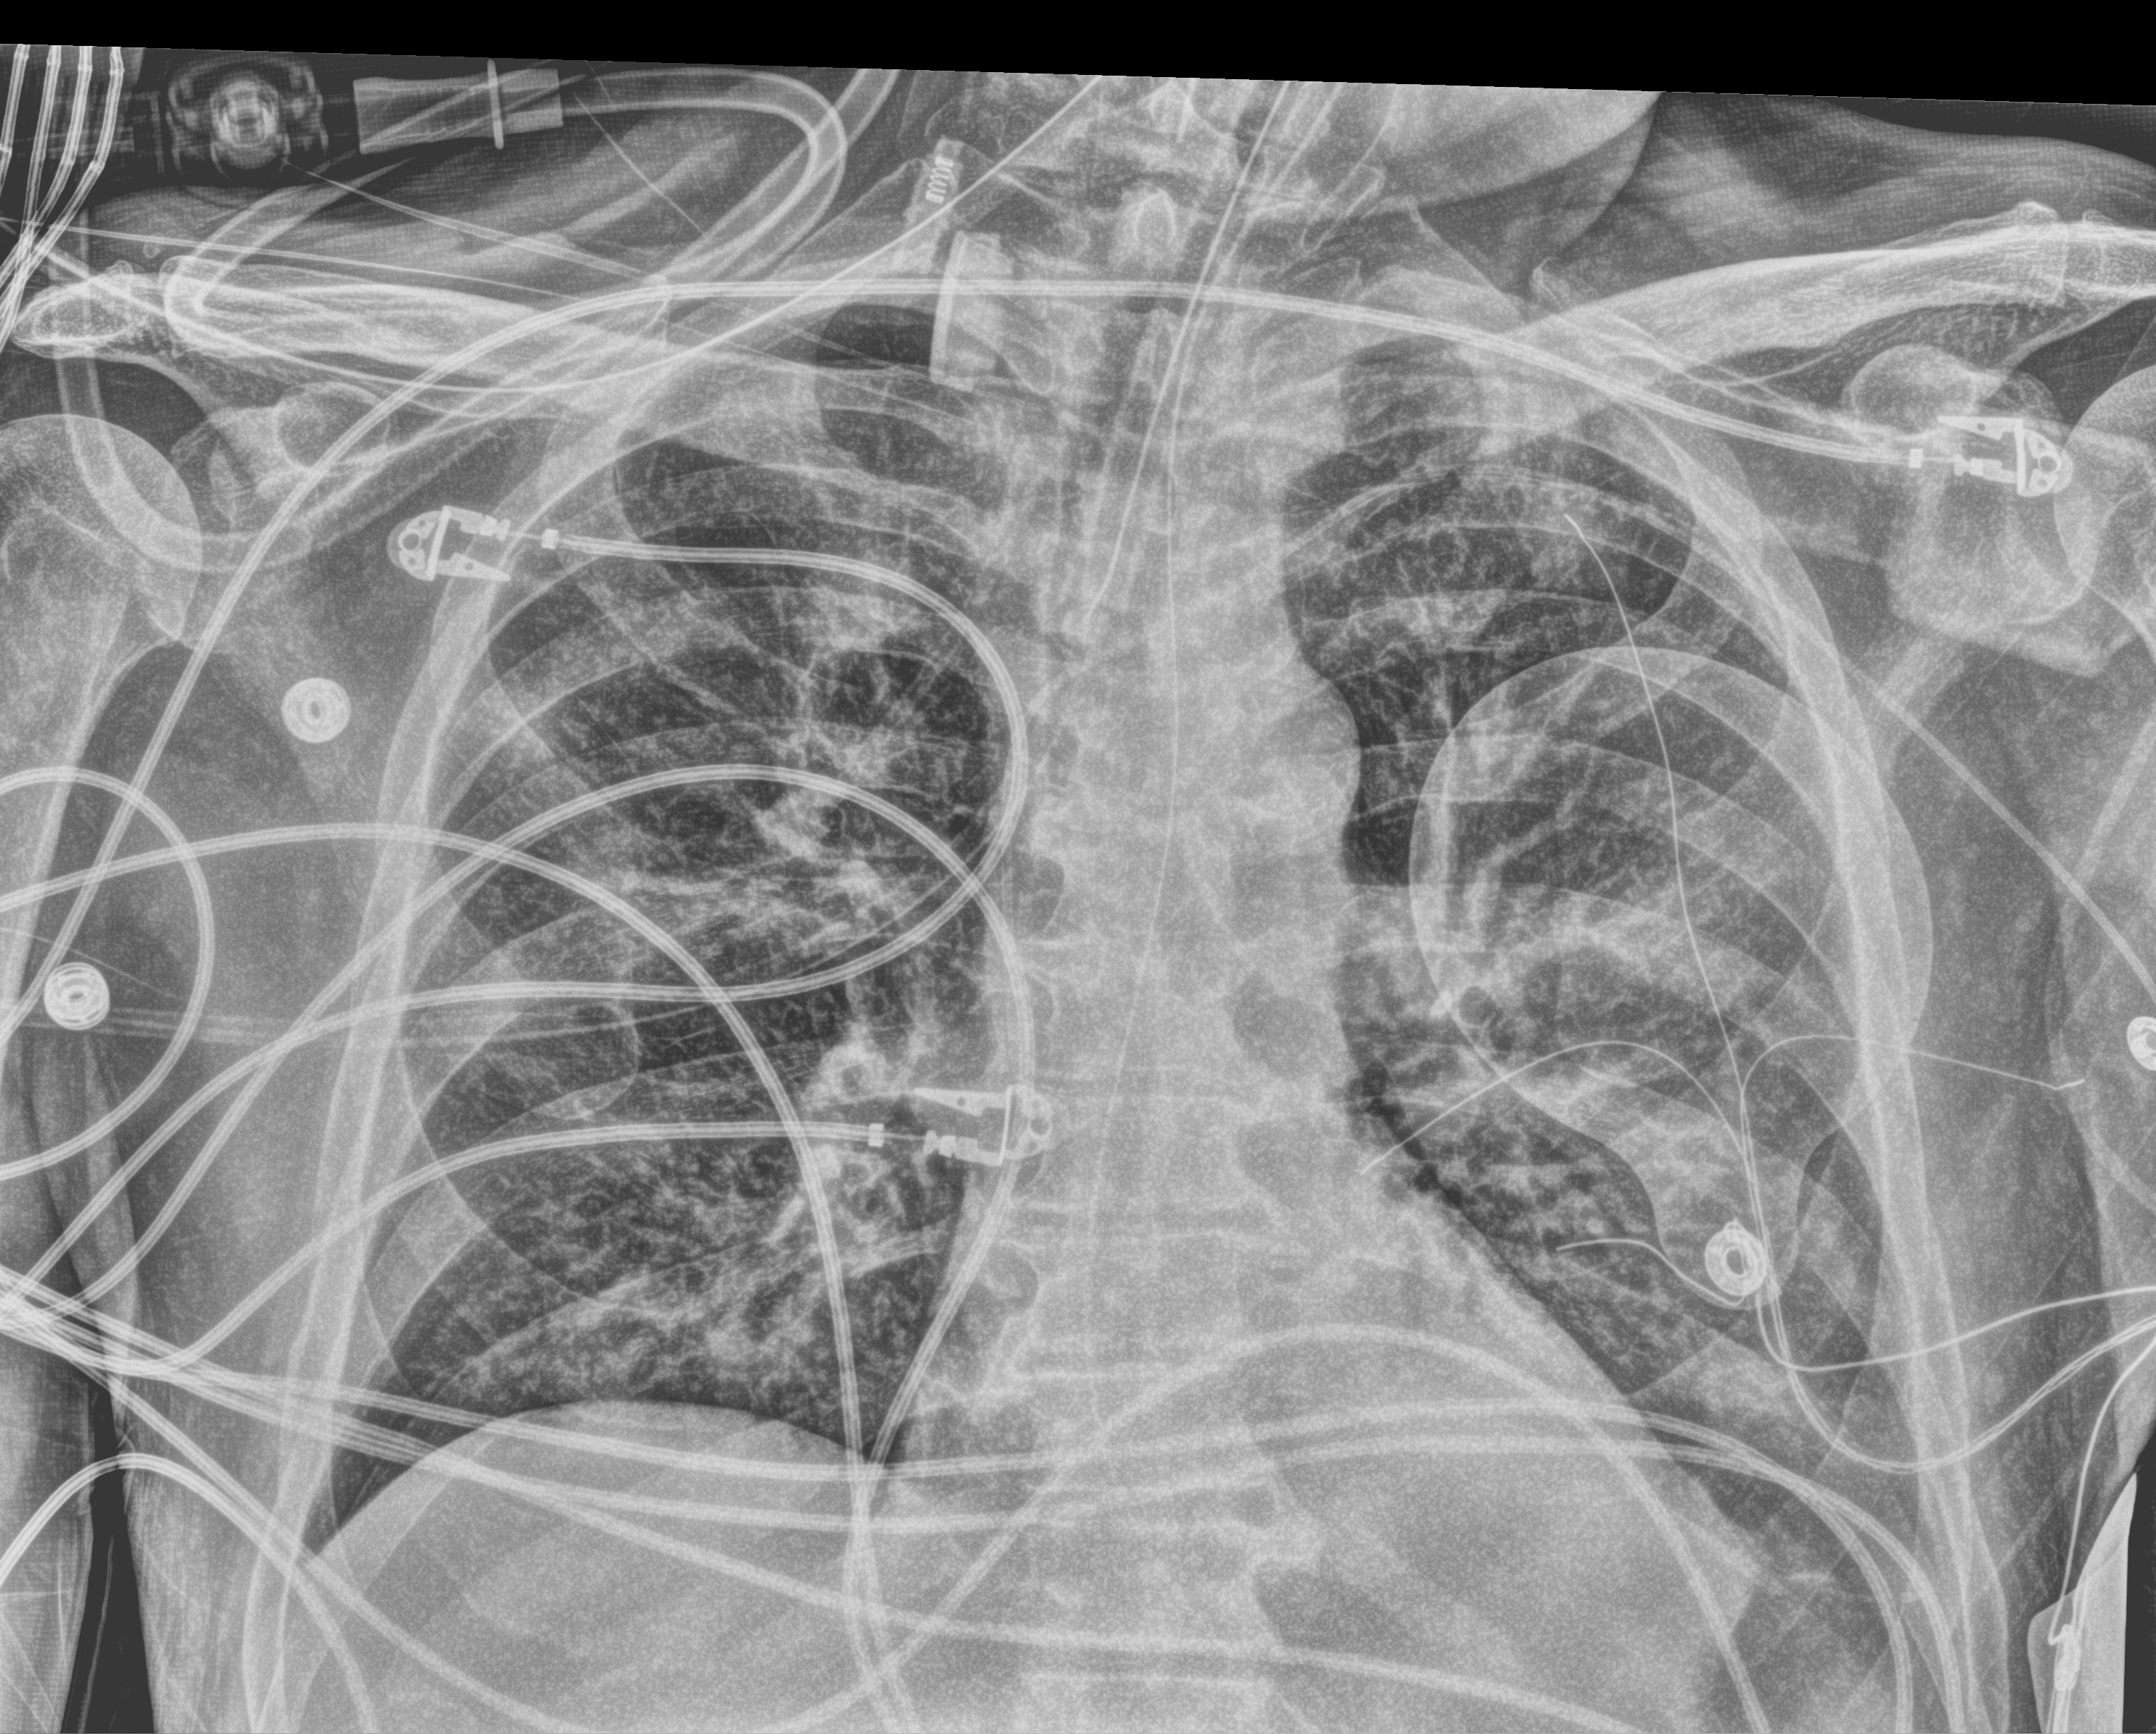
Bedside chest radiograph (computed radiography); anteroposterior (AP) projection. Patient hospitalised with COVID-19; male, aged 60–74 years.
From the hospital-stay record, not from the radiograph (when in the stay this image was taken is not recorded): admitted to intensive care during this hospital stay: yes; mechanically ventilated during this hospital stay: yes; other chronic lung disease (admission record): no.